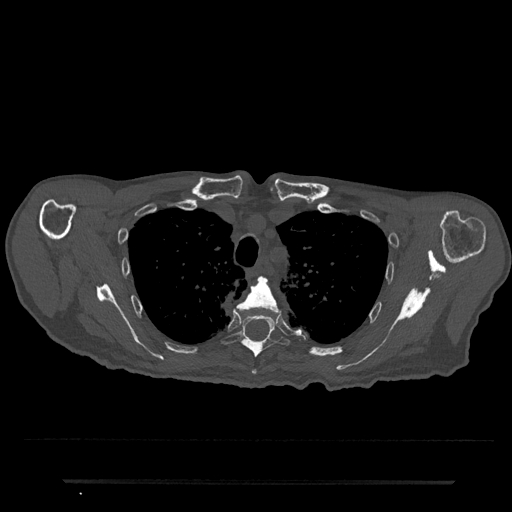
CT including the spine, one axial slice. Slice 592 of 797 in the series (ordered by position). Reconstruction kernel Br40s/3. 120 kVp. Bone window (W 1800 / L 400 HU). 0.5 mm slice thickness. 512 × 512 image matrix. Male patient, age 74 years. From the clinical record (not read from this slice): primary cancer: prostate.
Annotated regions visible in this slice (semi-automatic segmentation, software-assisted and operator-edited):
- T4 vertebra: bounding box <237,277,282,375> (left, top, right, bottom; pixels)
- T5 vertebra: <219,308,290,358>